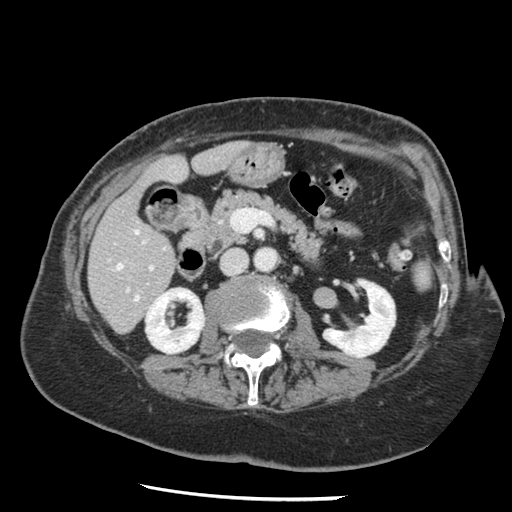
Contrast-enhanced abdominal CT, one axial slice. Position 56 of 148 along the scan axis. Reconstruction kernel STANDARD. 120 kVp. Intravenous contrast given. Soft-tissue window (W 400 / L 40 HU). 2.5 mm slice thickness. 512 × 512 image matrix, field of view 330 × 330 mm. Female patient, age 85 years. From the clinical record (not read from this slice): diagnosis: colorectal cancer liver metastases, imaged before liver resection; multiple liver metastases: no; largest metastasis: 0.9 cm; disease in both lobes: no.
Structures marked on this image (outlined manually by an expert reader):
- hepatic veins: bounding box [x1, y1, x2, y2] px = [117, 230, 139, 300]
- liver: [90, 143, 244, 333]
- planned liver remnant (the part of the liver to remain after resection): [90, 143, 244, 329]